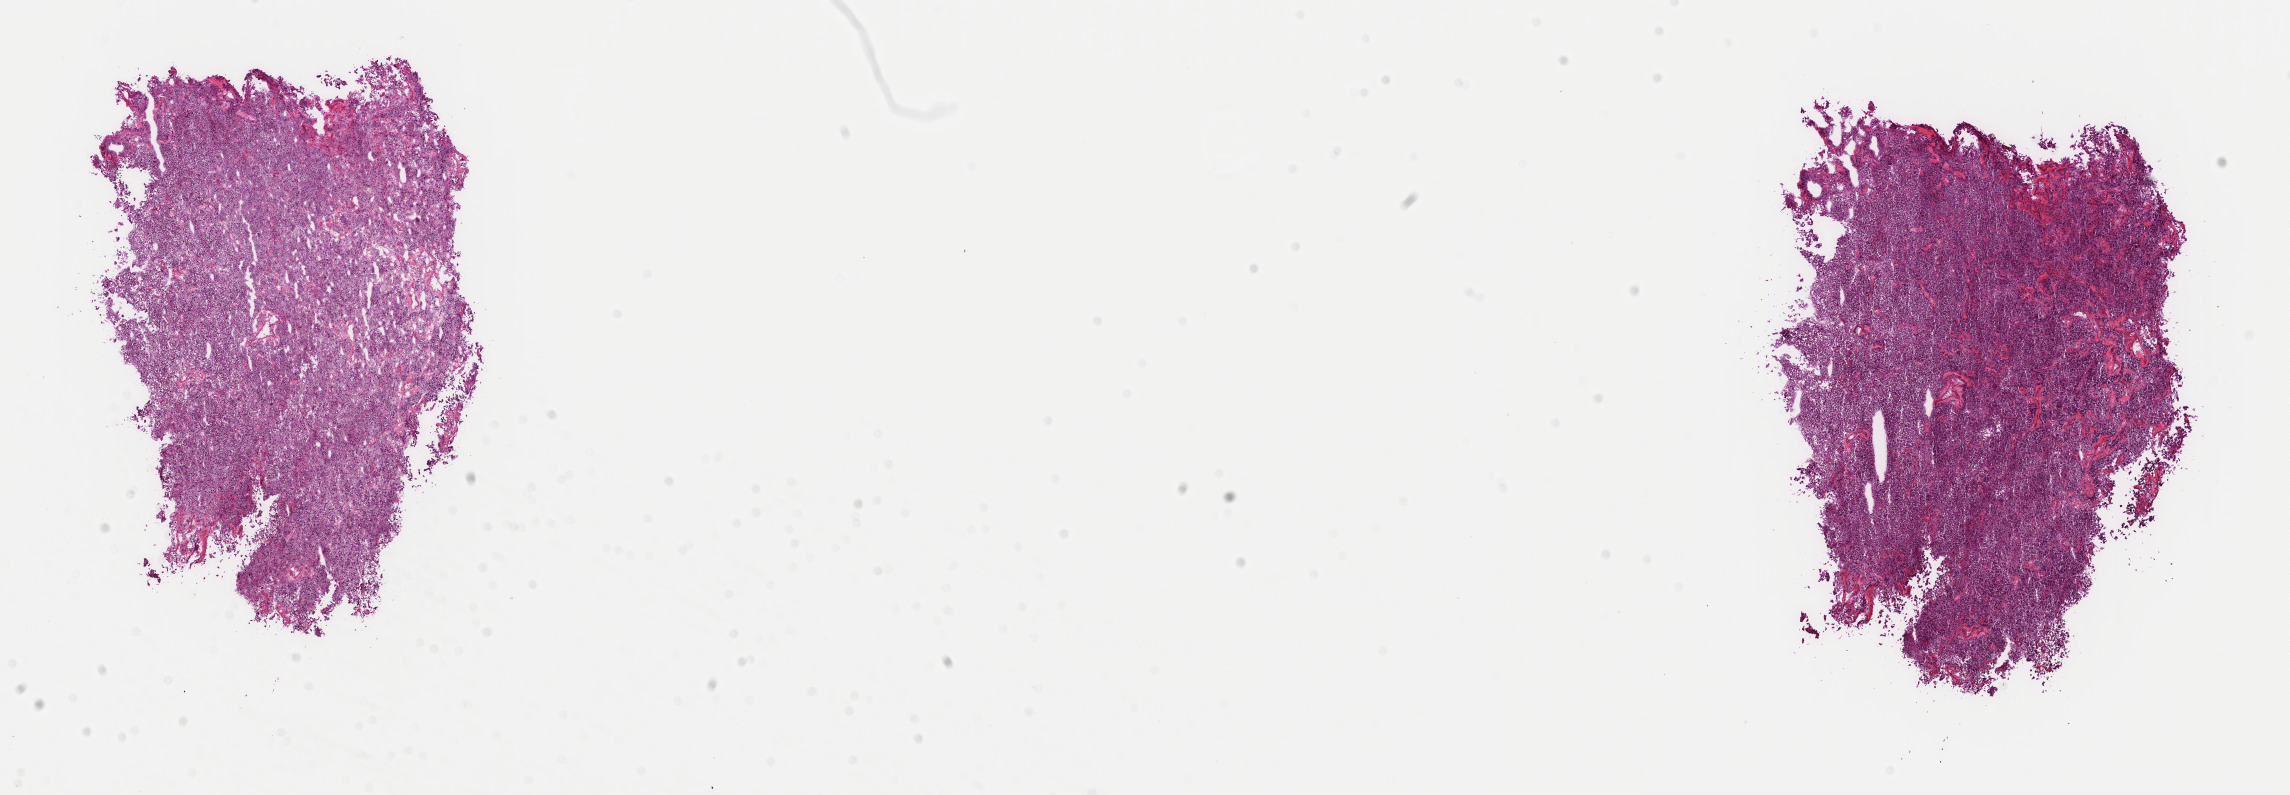
Whole-slide histology image, H&E, shown as a low-resolution overview of the whole scanned area (about 18.1 x 6.3 mm, acquisition: 40x scan); frozen section from the top of the tissue portion; primary tumour sample from the adrenal gland. Male, age 43 years at initial diagnosis. Pathologist review of this section (percent, as recorded): tumour cells 100%, tumour nuclei 95%, normal cells 0%, stromal cells 0%, necrosis 0%. Inflammatory infiltration, as recorded: lymphocyte infiltration 0%, monocyte infiltration 0%, neutrophil infiltration 0%.
Pathologic diagnosis: Pheochromocytoma, NOS.